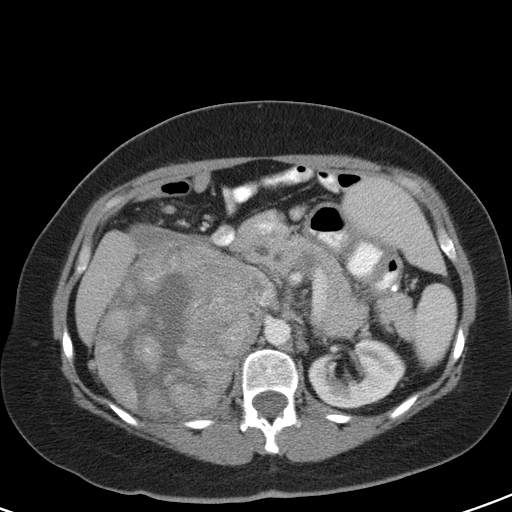
Contrast-enhanced abdominal CT, one axial slice; slice 68 of 126 in the series (ordered by position); 120 kVp; soft-tissue window (W 400 / L 40 HU); 512 × 512 image matrix. Female patient, age 51 years. Case-level facts recorded for this patient, not image findings: diagnosis: adrenocortical carcinoma; tumour side: right adrenal; tumour size at pathology: 17 cm; Ki-67 index: 12 %; stage (as recorded): 2.
Structures marked on this image (semi-automatically segmented with operator editing):
- mass: box from (x=96, y=231) to (x=260, y=420) px